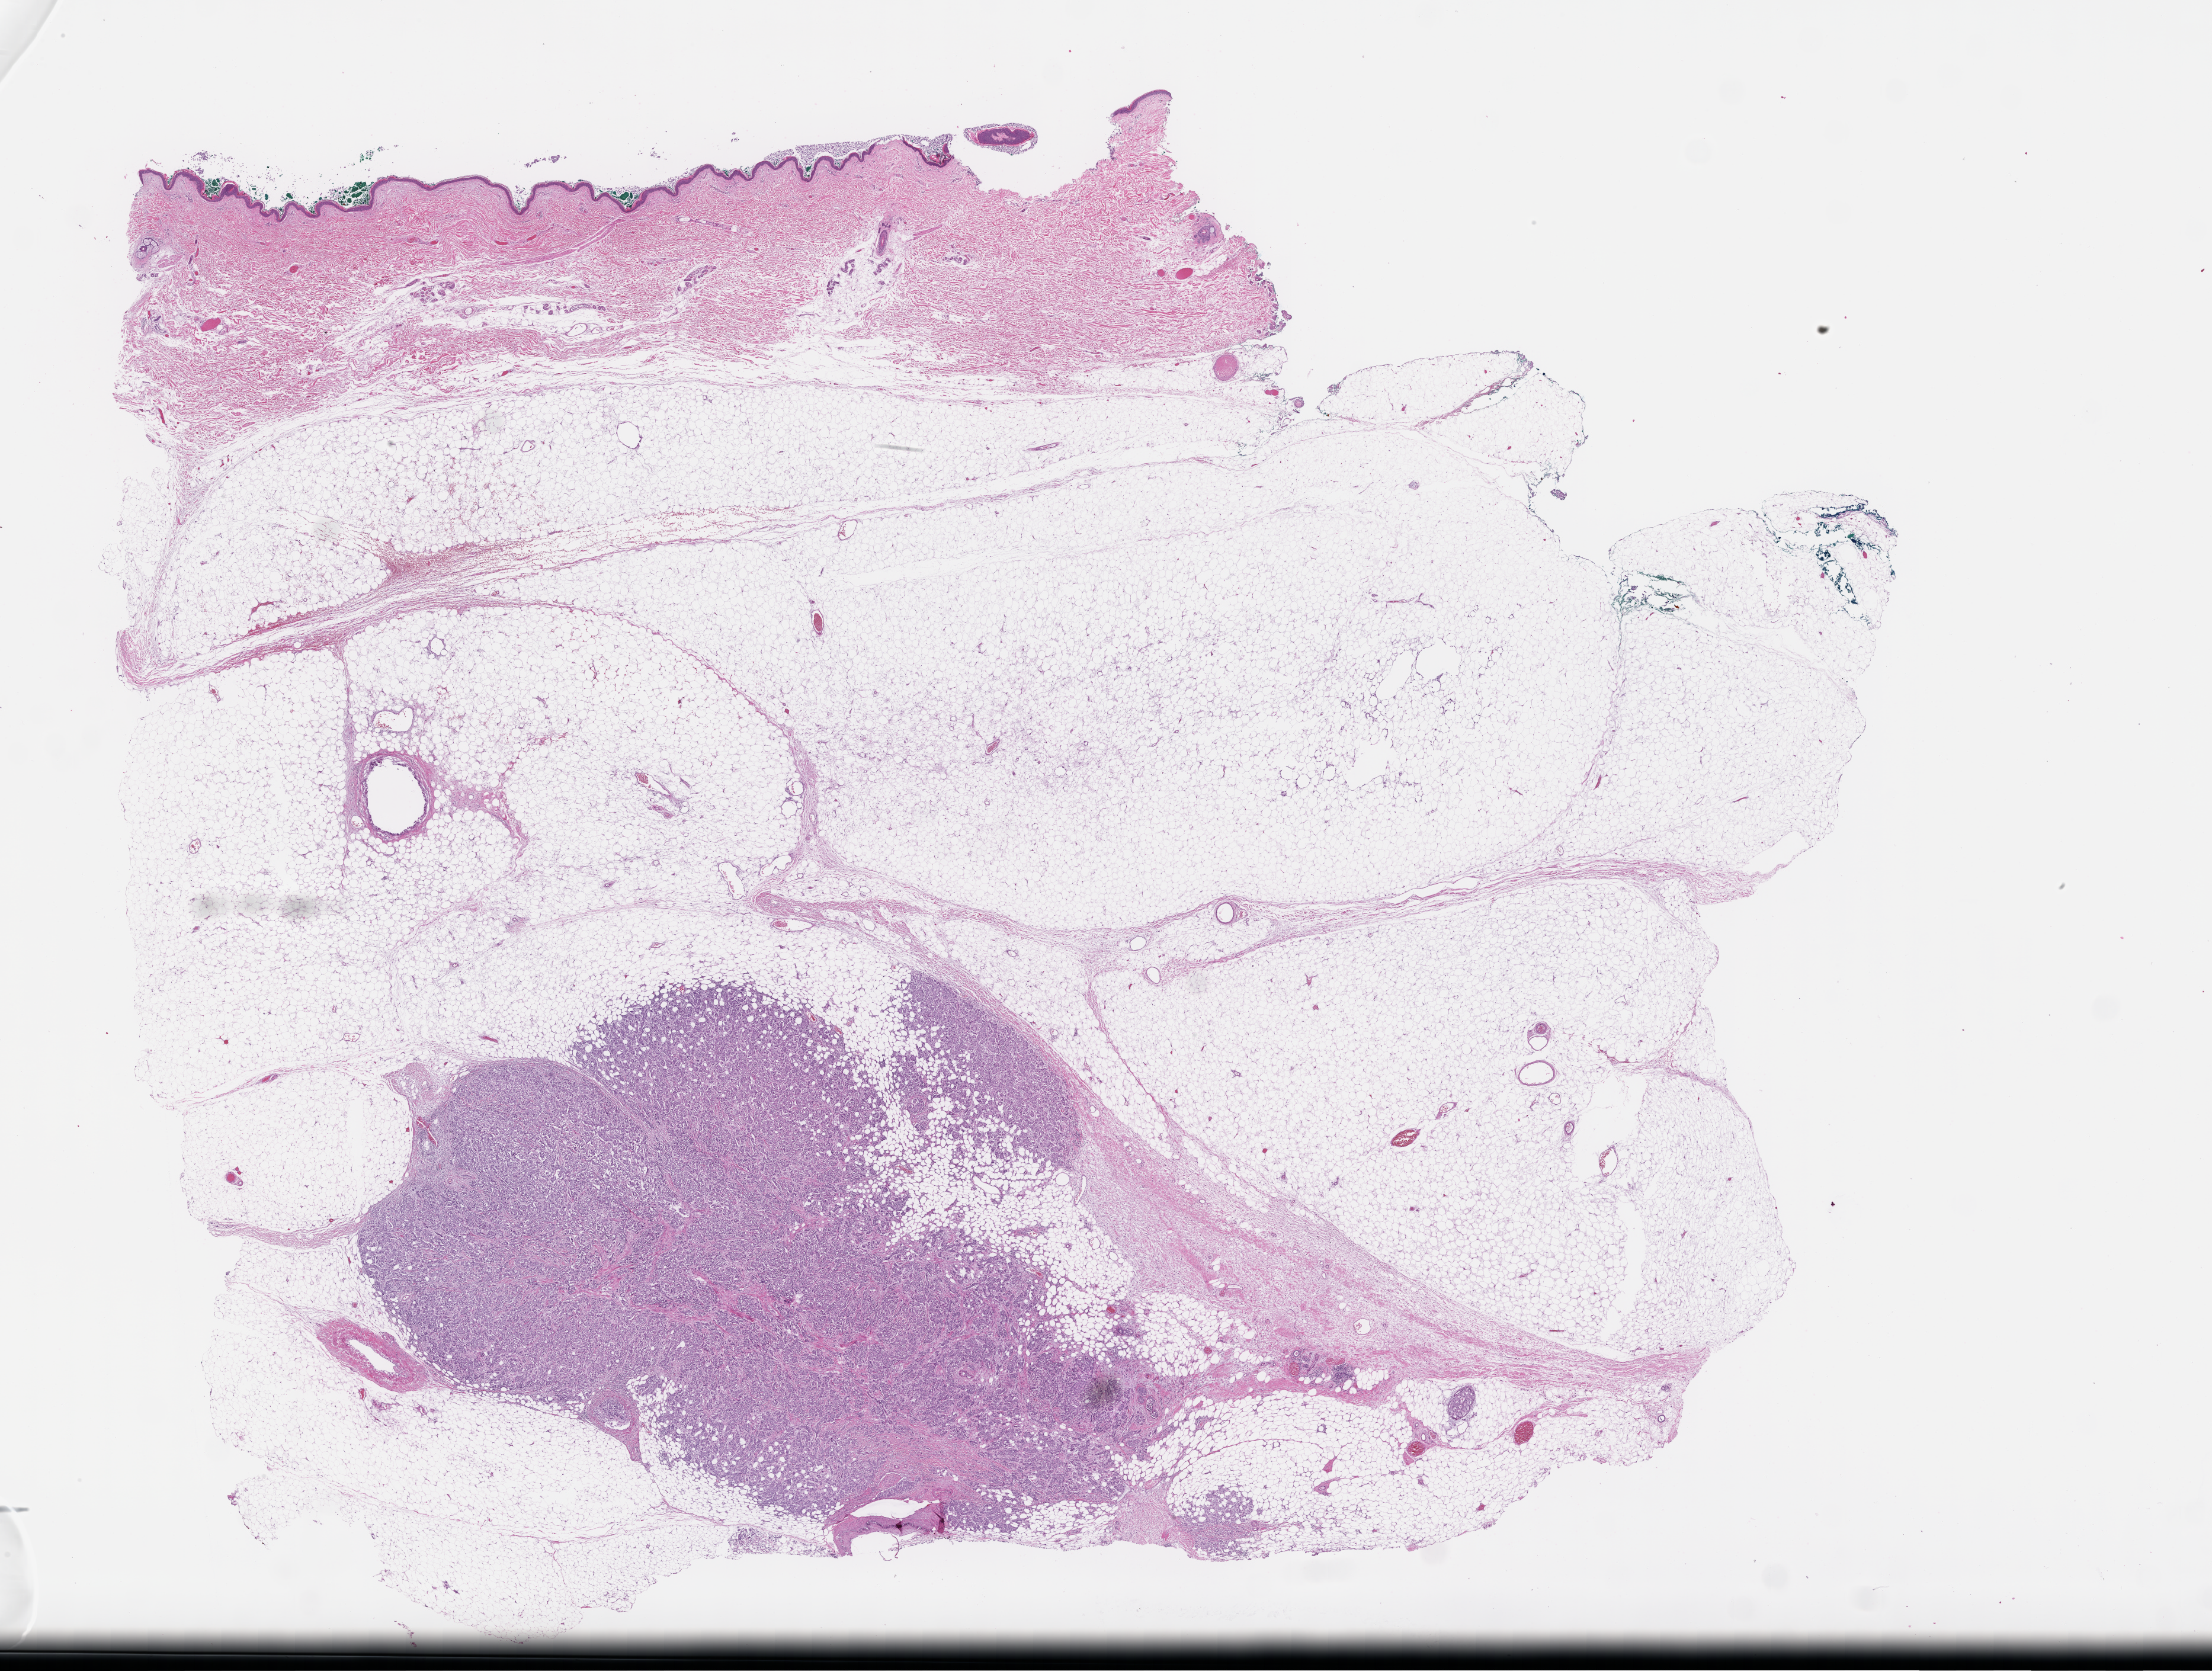
Digitized H&E-stained section, whole scanned area (about 30.2 x 22.8 mm) shown as a low-resolution overview, formalin-fixed paraffin-embedded section, site: breast. Female patient.
This section: primary tumor. Diagnosis: Invasive Breast Carcinoma.